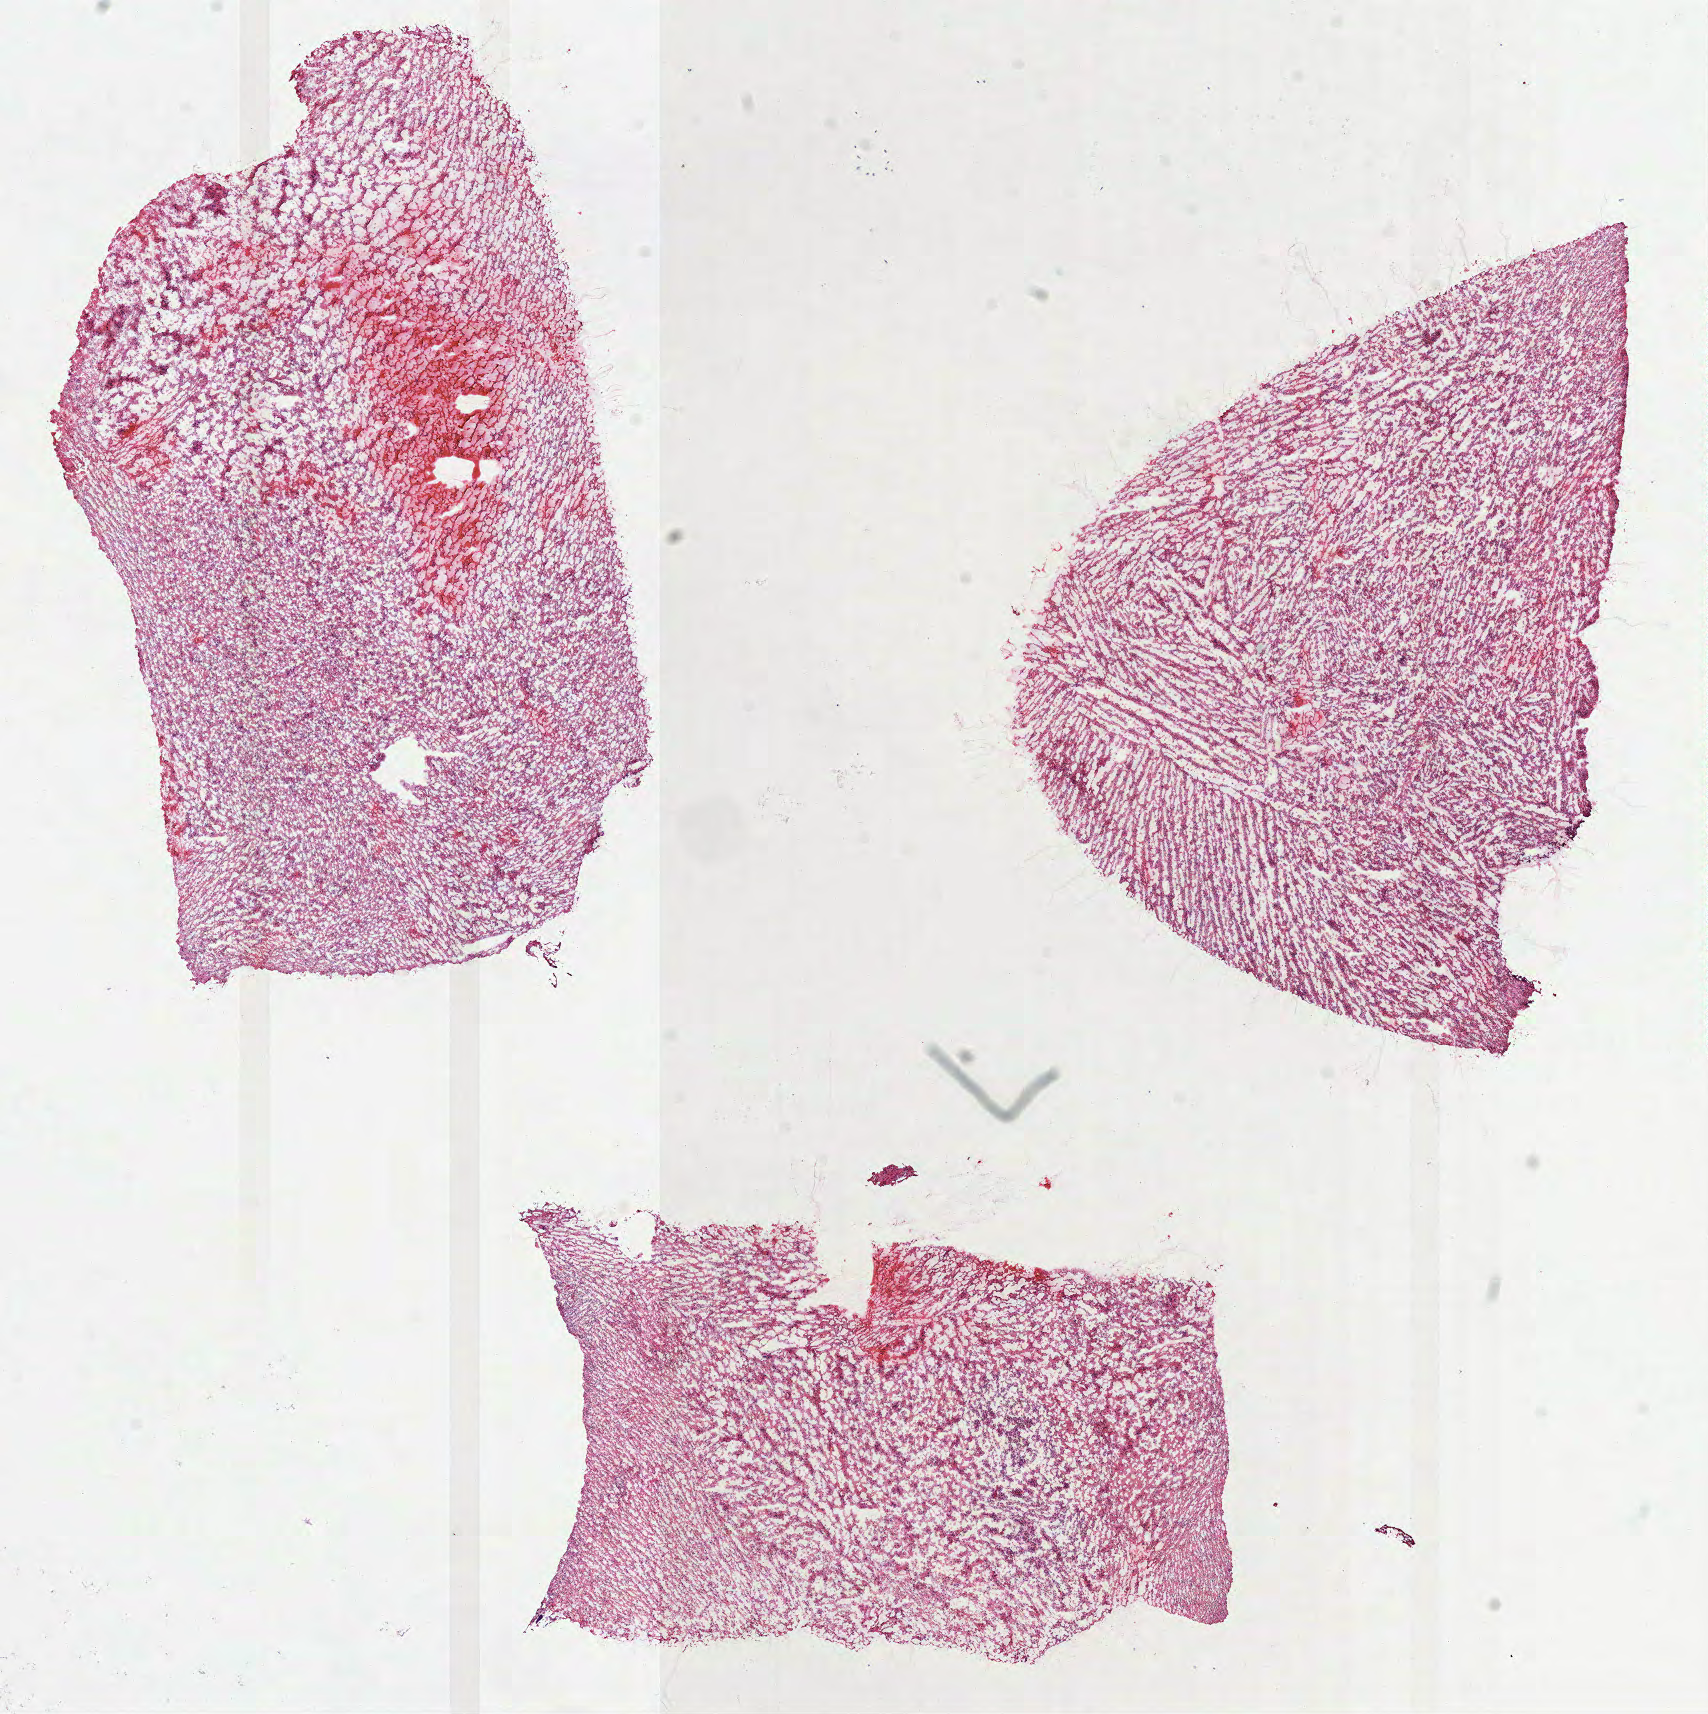
Whole-slide histology image, Hematoxylin and eosin (H&E) stained — shown as a low-resolution overview of the whole scanned area (about 13.8 x 13.8 mm); frozen section from the top of the tissue portion; brain, primary tumour sample. Female, age 64 years at initial diagnosis. Composition of this section per pathologist review: tumour cells 100%, tumour nuclei 80%, normal cells 0%, stromal cells 0%, necrosis 0%.
Histologic diagnosis: Glioblastoma.